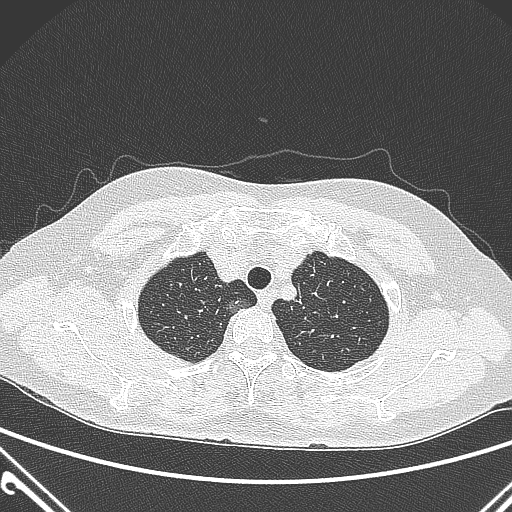
Chest CT, one axial slice; position 243 of 300 along the scan axis; 120 kVp; lung window (W 1500 / L -600 HU); 1 mm slice thickness; 512 × 512 image matrix, field of view 350 × 350 mm. Patient: female, 54 years. From the clinical record (not read from this slice): clinical TNM (as recorded): T1a N0 M0.
Structures marked on this image (rectangle marked by the reading radiologist):
- lung tumour (recorded histology: adenocarcinoma): bounding box <220,297,256,318> (left, top, right, bottom; pixels)